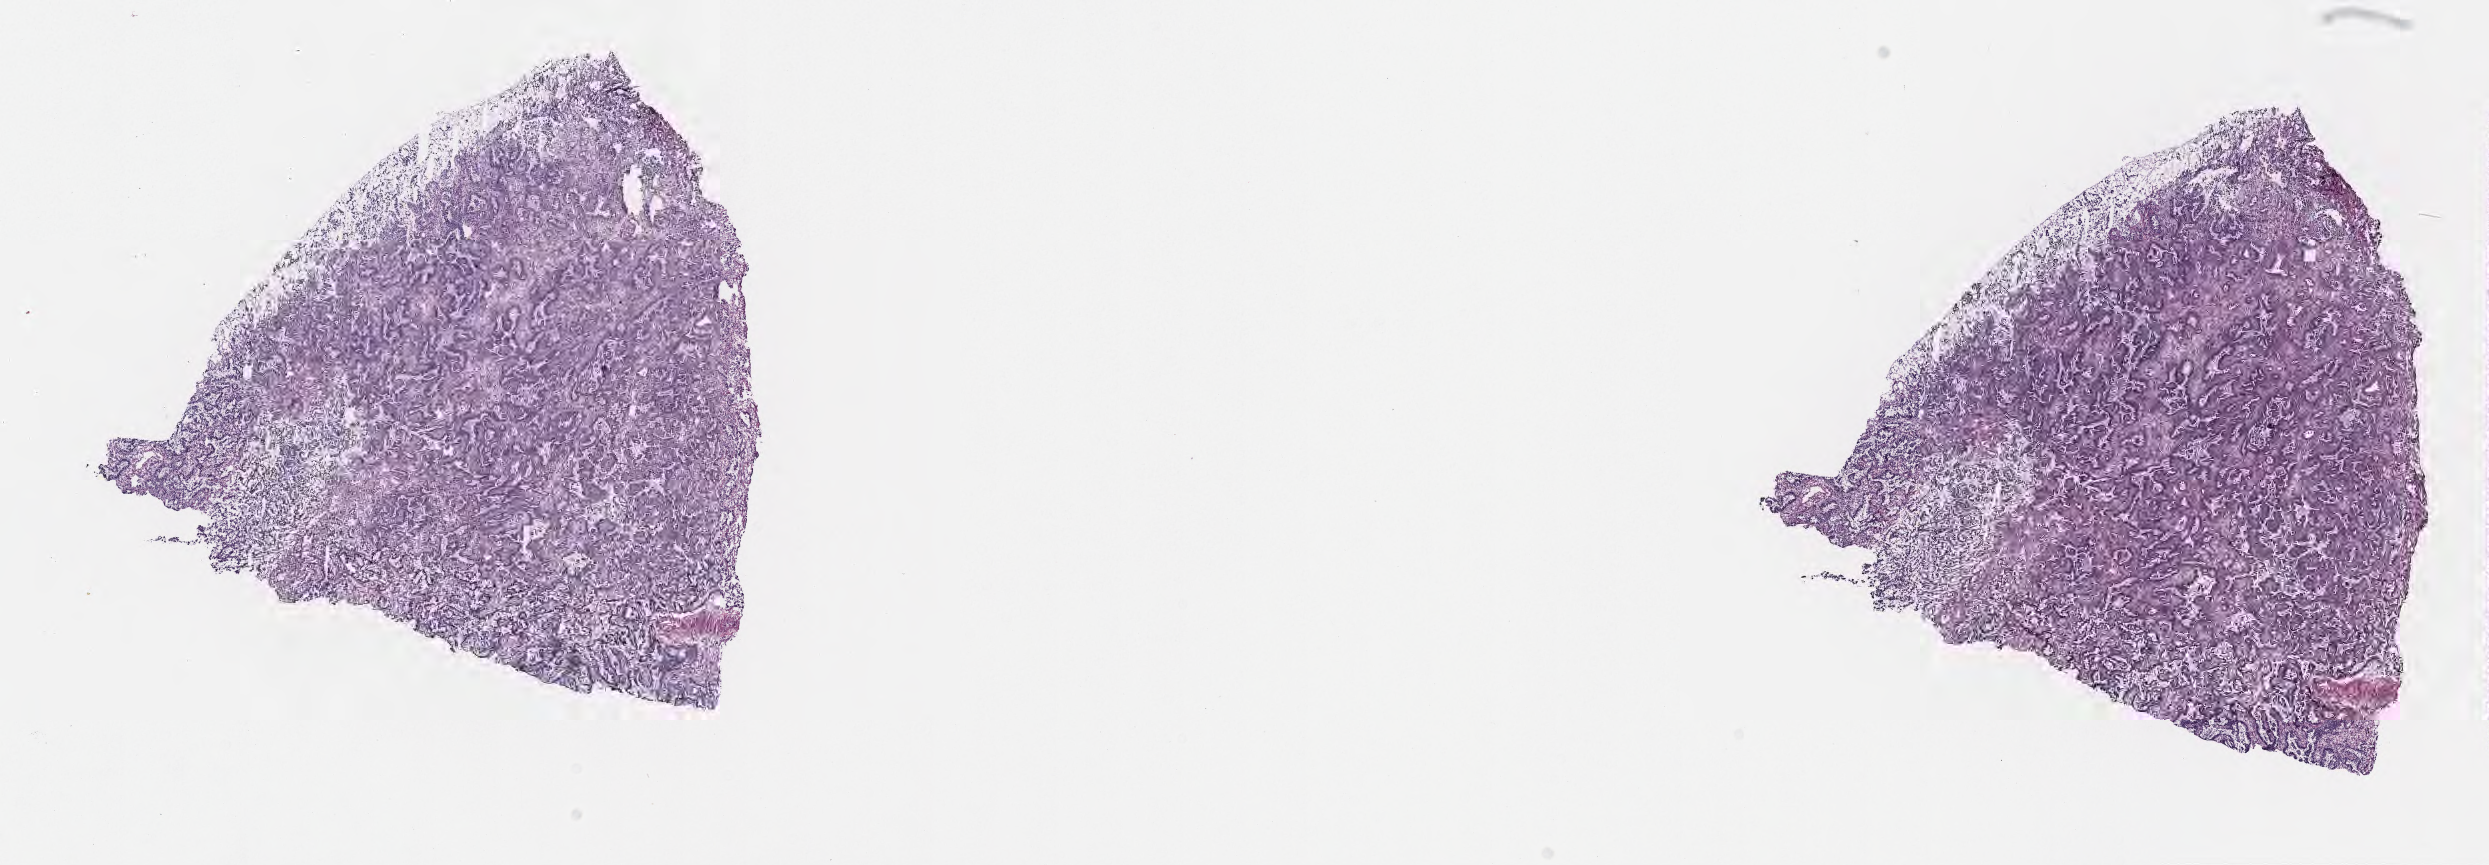
Whole-slide image, H&E stain, a low-resolution overview of the entire scanned area, about 20.1 x 7.0 mm. Frozen section (tissue freezing medium). Primary tumor. Anatomic site: upper lobe of right lung. Patient: male, age 73 years. Pathologist review of this section (percent, as recorded): tumor cells 70%, tumor nuclei 70%, stromal cells 27%, necrosis 1%, normal cells 2%. Inflammatory infiltration, as recorded: lymphocyte infiltration 5%, monocyte infiltration 5%, neutrophil infiltration 6%.
AJCC pathologic stage: Stage IIIA. Histologic diagnosis: Adenocarcinoma, NOS.